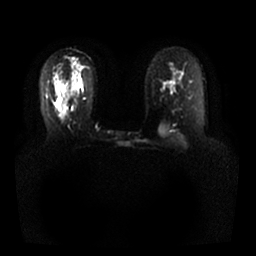
Breast MRI, one axial slice; slice 16 of 25 in the series (ordered by position); diffusion-weighted series; image 2 of 4 stored at this slice position (different b-values; order by instance number); 1.5 T; 4 mm slice thickness; 256 × 256 image matrix, field of view 350 × 350 mm. Female patient.
Structures marked on this image (manually delineated by an expert):
- tumour on diffusion-weighted imaging: box from (x=59, y=103) to (x=64, y=115) px